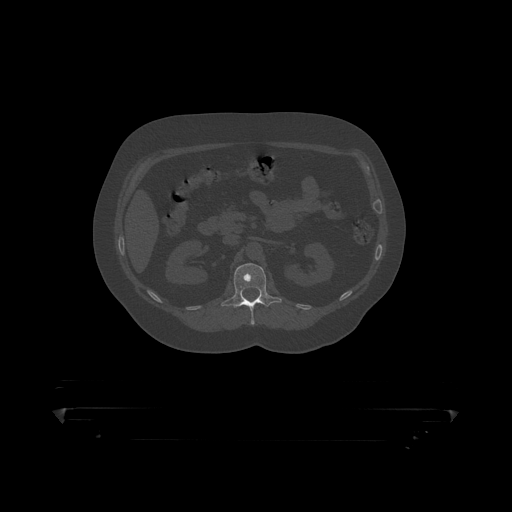
CT including the spine, one axial slice. Slice 148 of 390 in the series (ordered by position). Reconstruction kernel STANDARD. Bone window (W 1800 / L 400 HU). 1.25 mm slice thickness. 512 × 512 image matrix, field of view 650 × 650 mm. Male patient, age 60 years. From the clinical record (not read from this slice): primary cancer: prostate.
Structures marked on this image (semi-automatic segmentation, software-assisted and operator-edited):
- L1 vertebra: bounding box <221,264,282,319> (left, top, right, bottom; pixels)